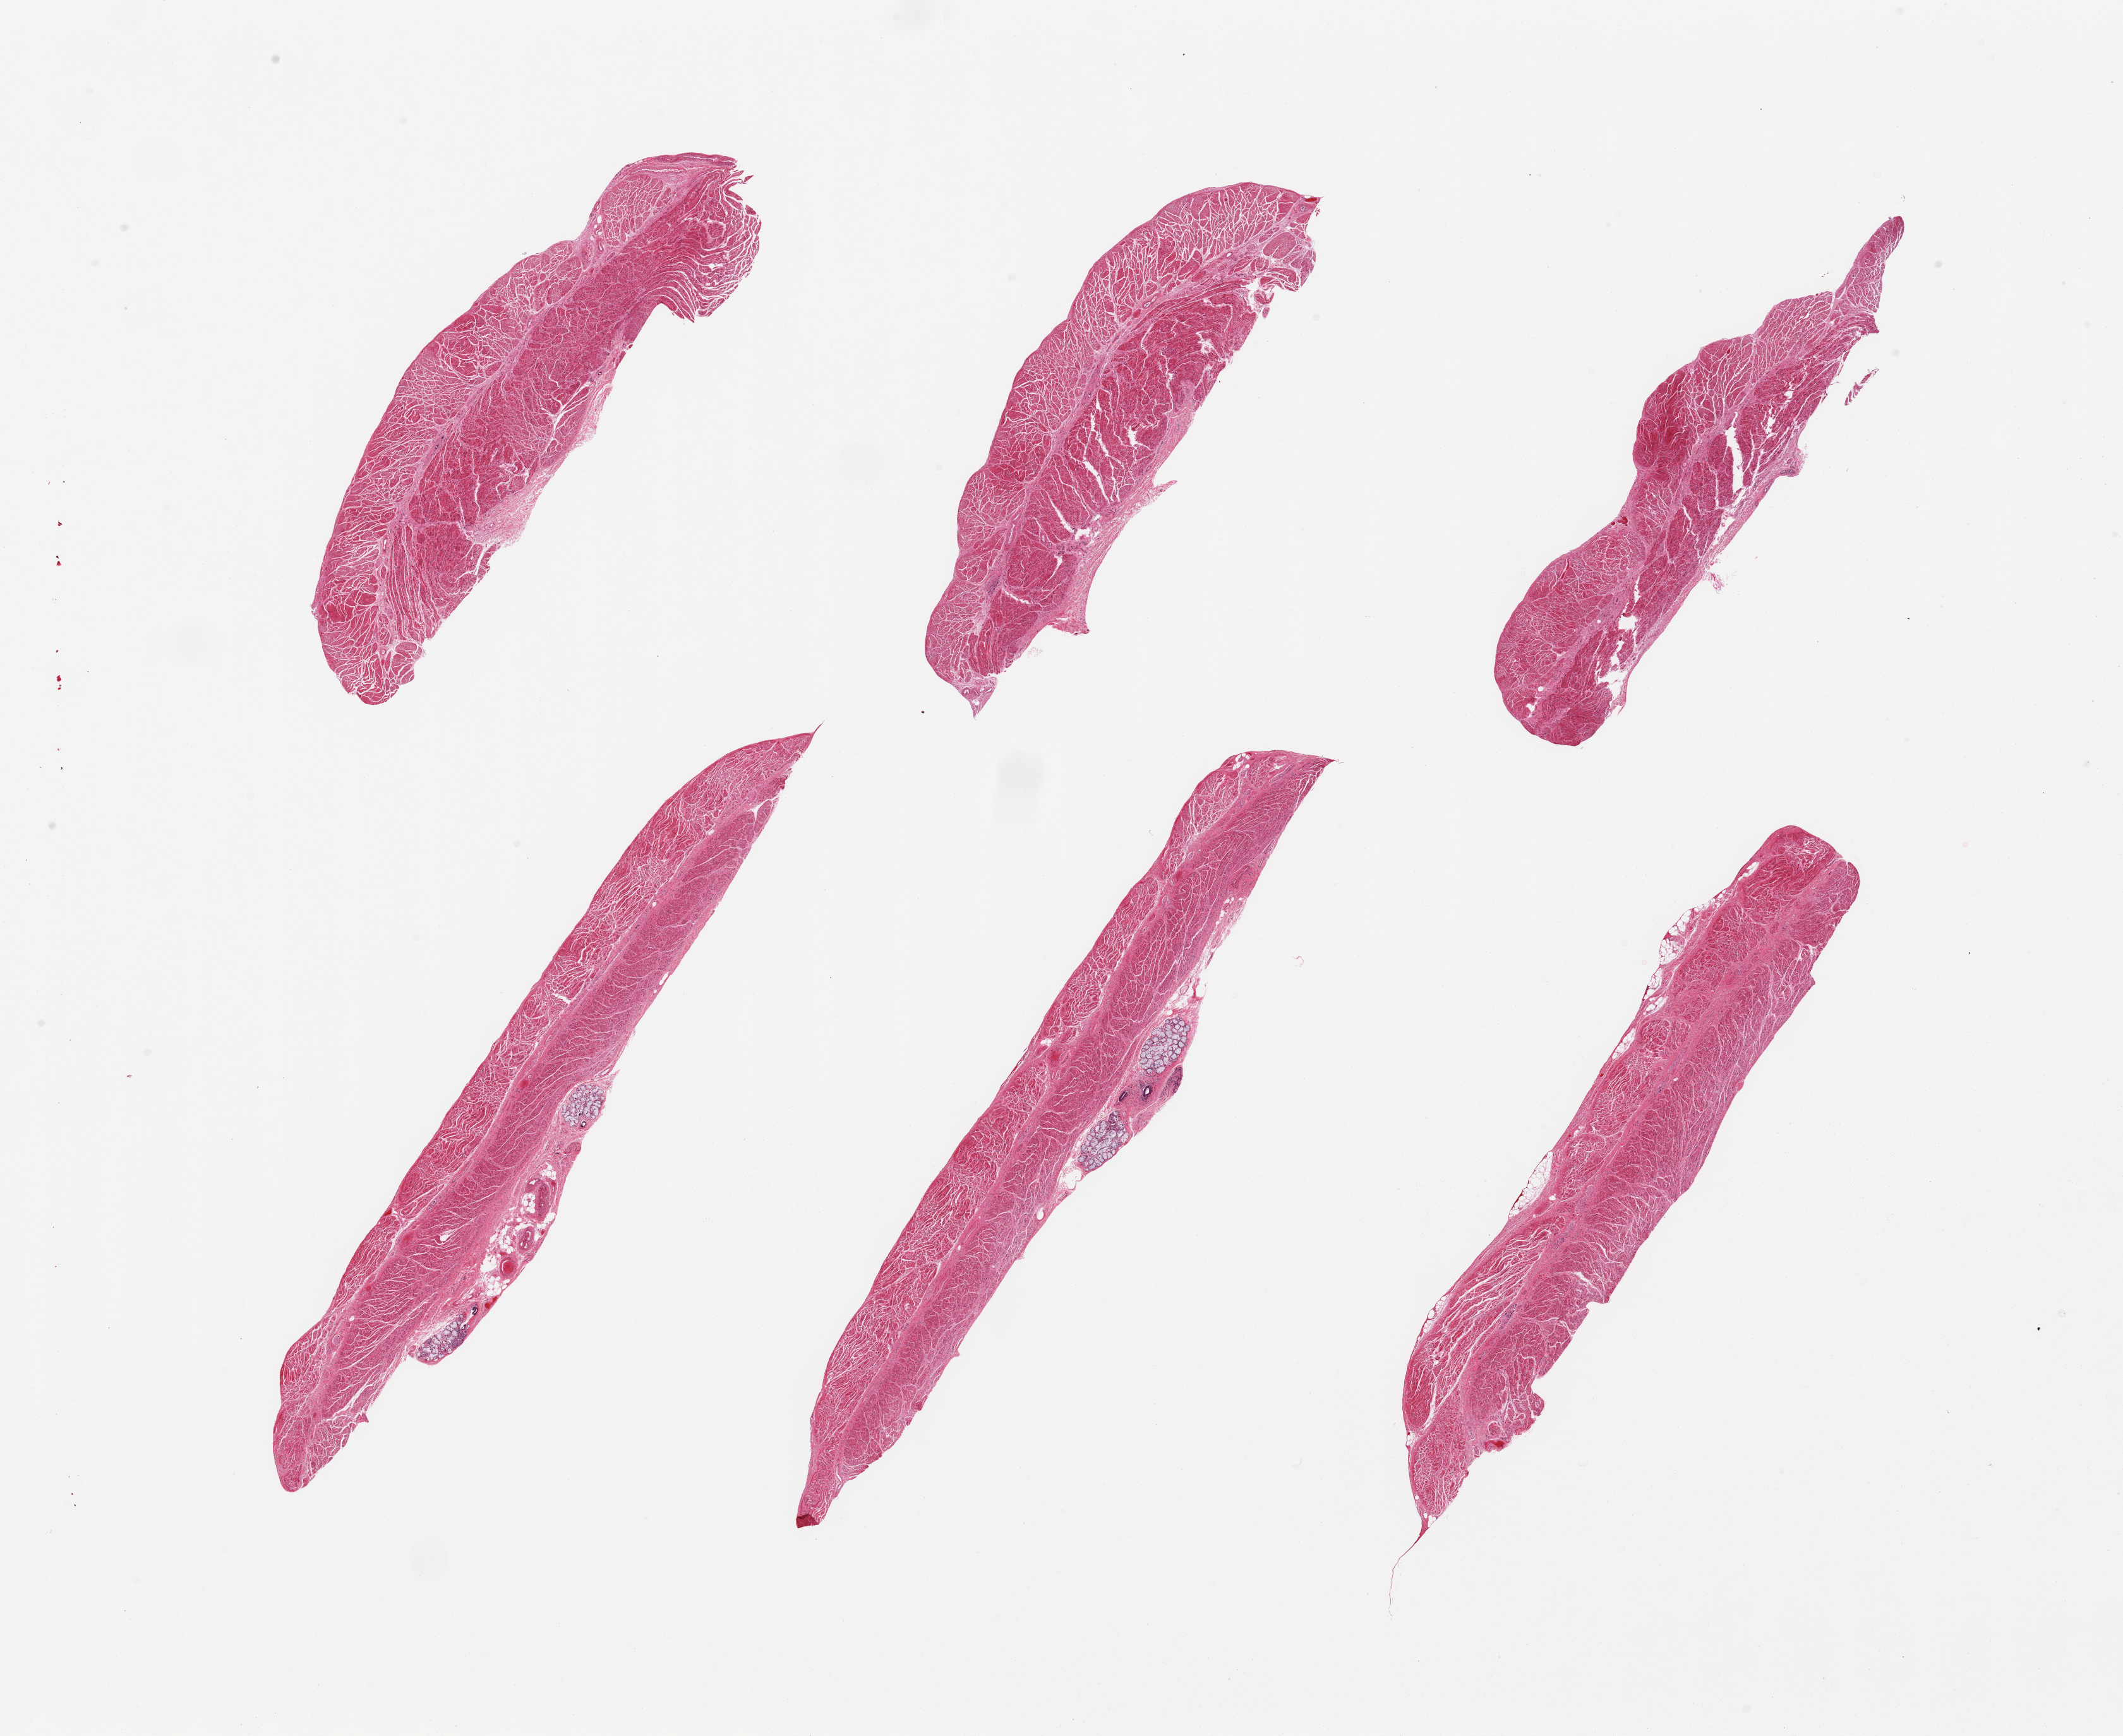
Haematoxylin and eosin whole-slide image, brightfield — shown as a low-resolution overview of the whole scanned area (about 26.6 x 21.7 mm, from a 20x scan). PAXgene-fixed paraffin-embedded (PFPE) section. Target tissue: gastroesophageal junction. Tissue donor sample. Male donor.
Reviewer comment on this tissue sample: 6 pieces; target muscularis and two pieces with rim of submucosa and submucosal glands.